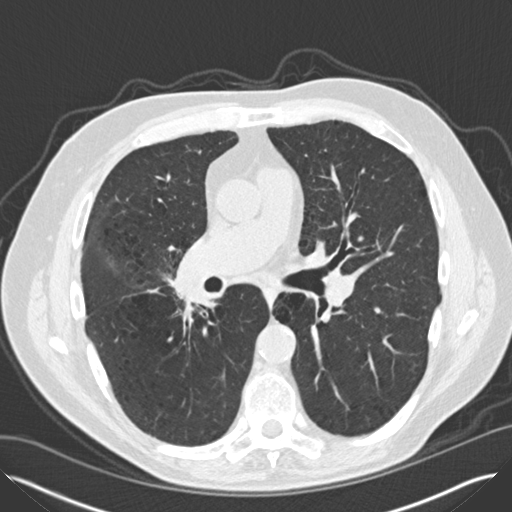
Low-dose screening chest CT, one axial slice. Position 78 of 149 along the scan axis. Reconstruction kernel B30f. 120 kVp. Lung window (W 1500 / L -600 HU). 2 mm slice thickness. 512 × 512 image matrix.
Structures marked on this image (manually delineated by an expert):
- lesion 2 (tumor, hilum of right lung): bounding box [x1, y1, x2, y2] px = [188, 277, 209, 303]